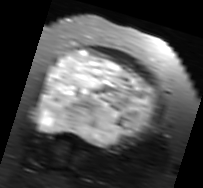
MRI of an extremity soft-tissue mass, one axial slice; slice 46 of 91 in the series (ordered by position); T2-weighted fat-saturated; MR volume resampled by the dataset authors to the PET/CT grid (not the native acquisition matrix); 3.27 mm slice thickness; 203 × 188 image matrix, field of view 198 × 184 mm. Female patient. From the clinical record (not read from this slice): histological type: malignant solitary fibrous tumor; grade: intermediate; site of the primary tumour: right thigh.
Structures marked on this image (expert contour drawn on MRI and transferred to this co-registered scan by the dataset authors):
- gross tumour volume including surrounding oedema: bounding box <30,49,159,148> (left, top, right, bottom; pixels)
- gross tumour volume (mass): <35,49,157,146>